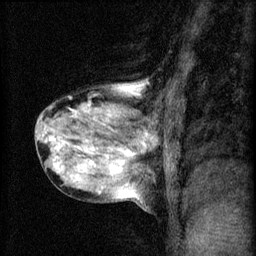
Breast MRI (dynamic contrast-enhanced), one sagittal slice. Position 27 of 60 along the scan axis. 3 images stored at this slice position (order not interpretable as contrast timing). 1.5 T. TE 4.2 ms, TR 8.2 ms. 2 mm slice thickness. 256 × 256 image matrix, field of view 180 × 180 mm. Female patient, age 40 years.
Outlined on this slice (semi-automatically segmented with operator editing):
- analysis volume of interest (the breast-tissue region the enhancement analysis was run in; not a lesion): box from (x=34, y=80) to (x=167, y=211) px
- tumour enhancement mask (voxels above the 70 % enhancement threshold inside the analysis volume of interest): (x=50, y=88)–(x=149, y=181)